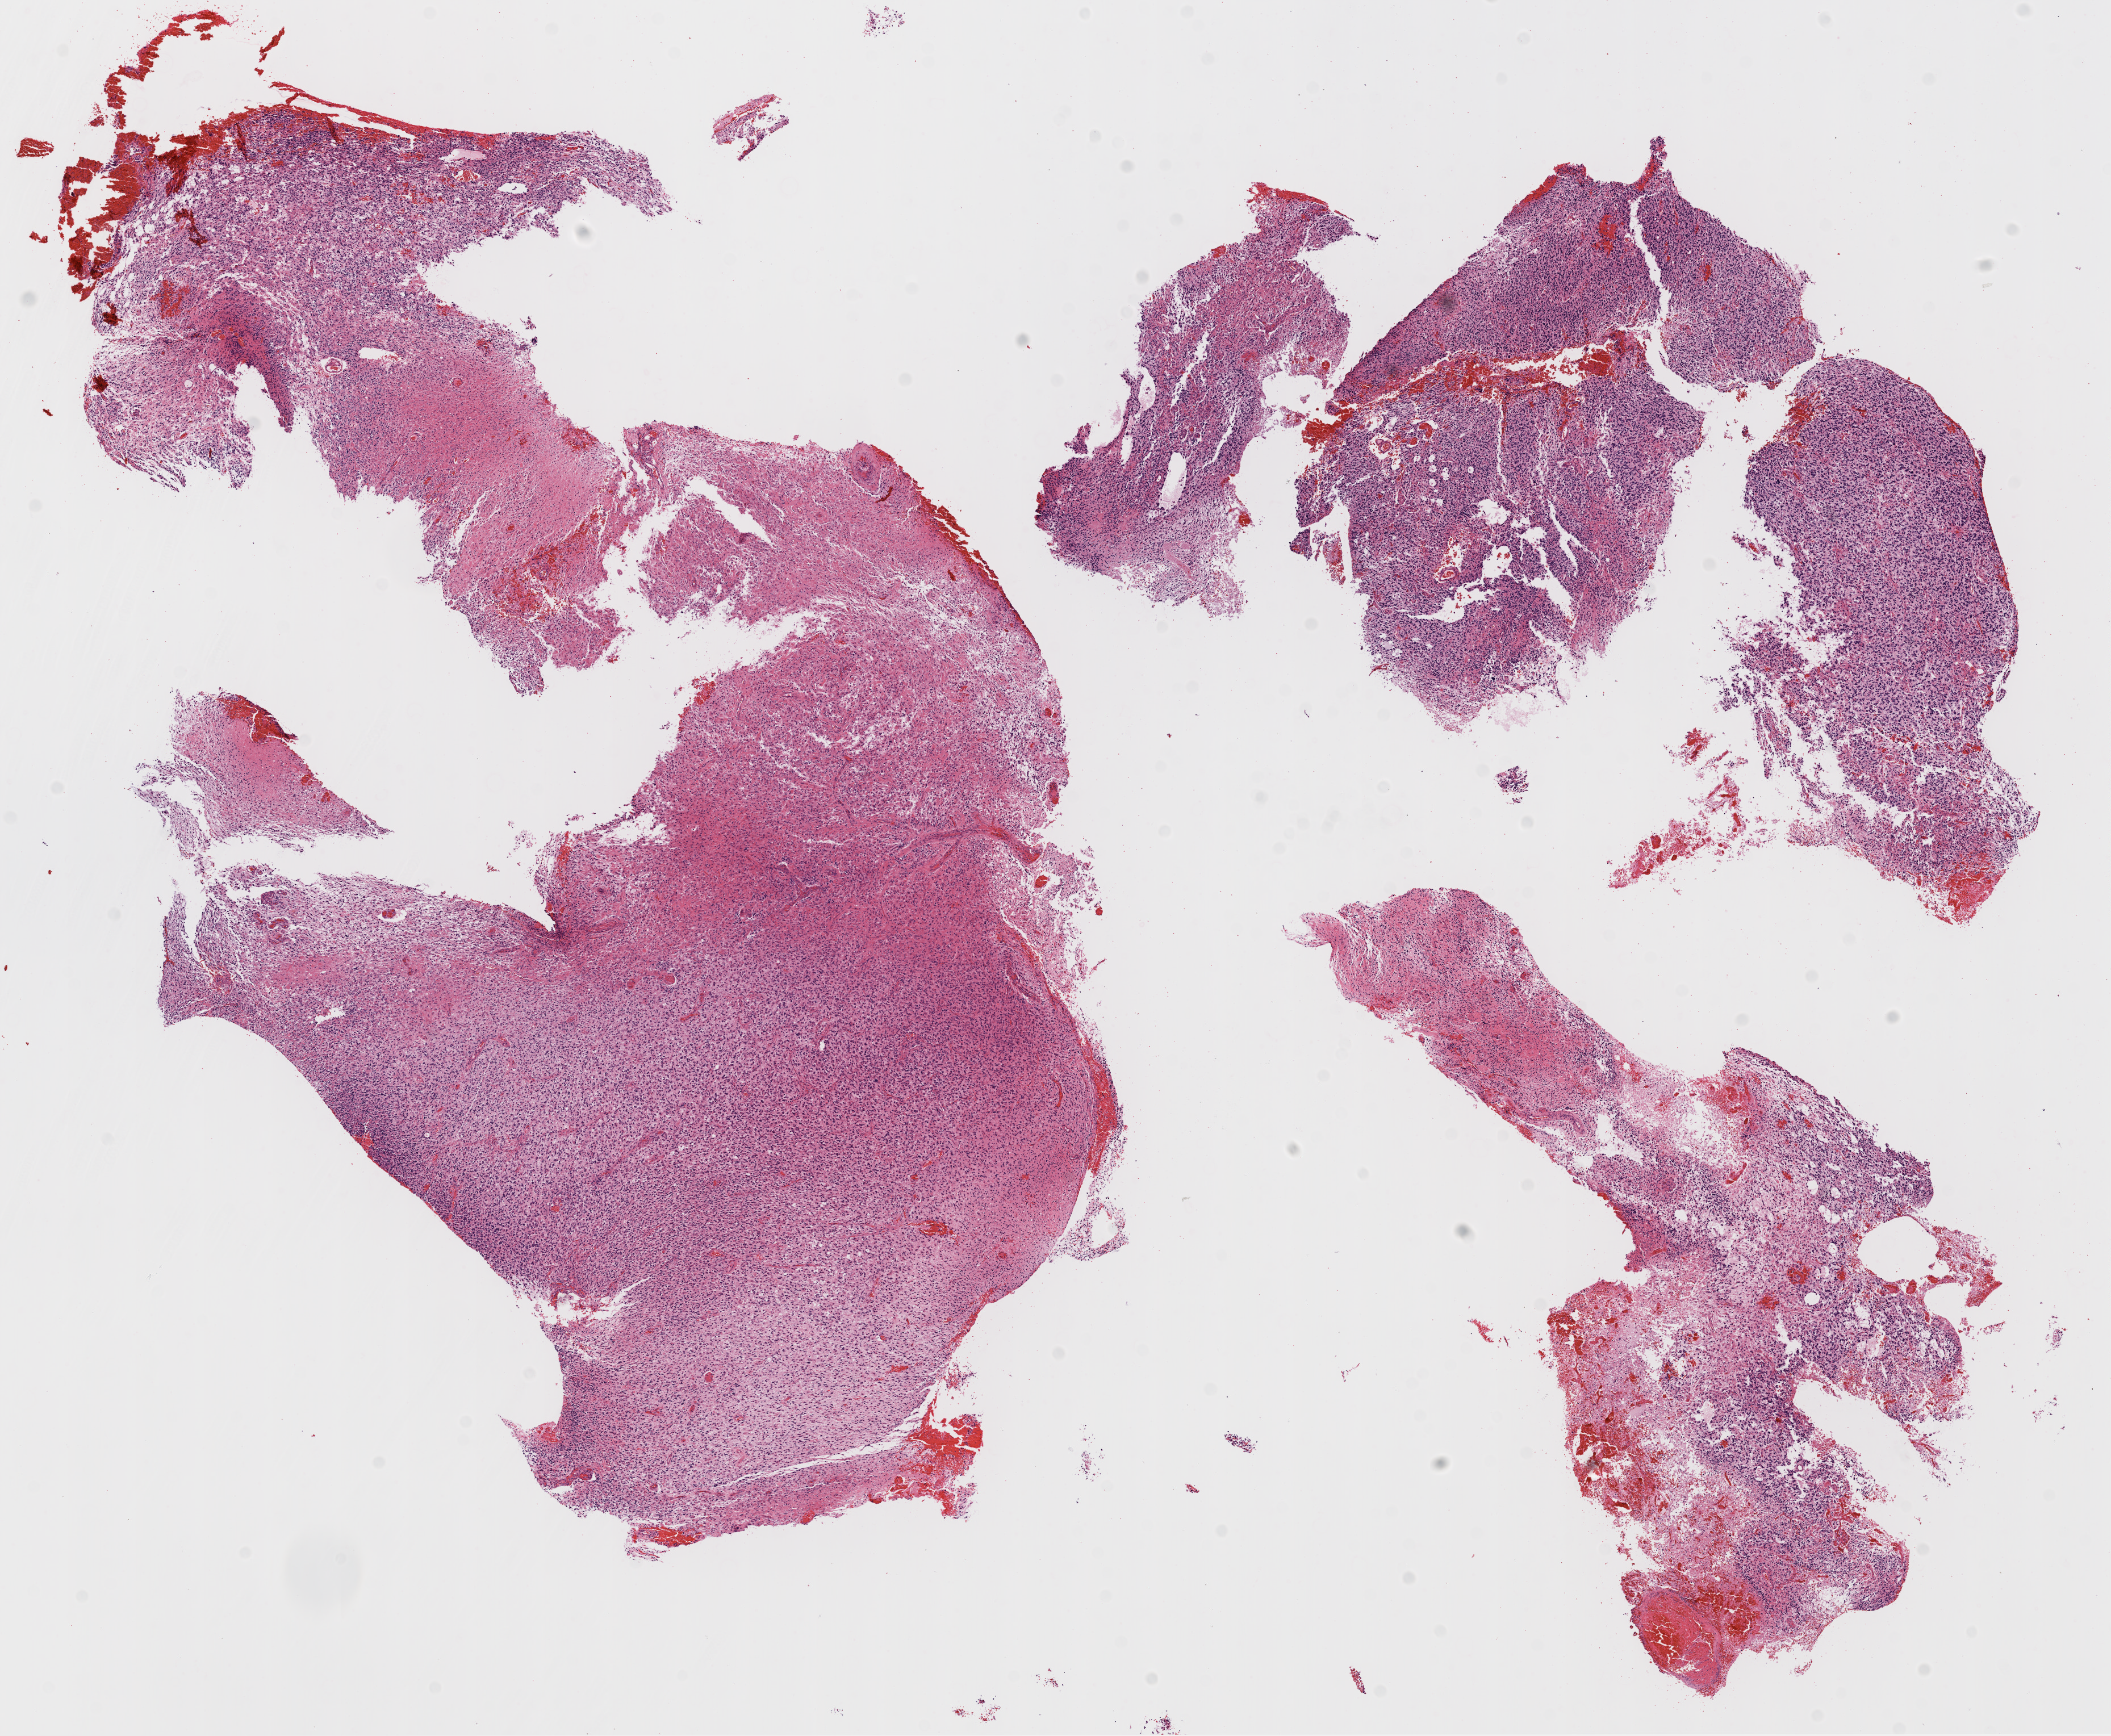
H&E whole-slide image — whole scanned area (about 15.0 x 12.3 mm, acquisition: 20x scan) shown as a low-resolution overview. Formalin-fixed paraffin-embedded (FFPE) diagnostic section. Sample: primary tumour, brain. Male patient; age at initial diagnosis 31 years.
Histologic diagnosis: Glioblastoma.